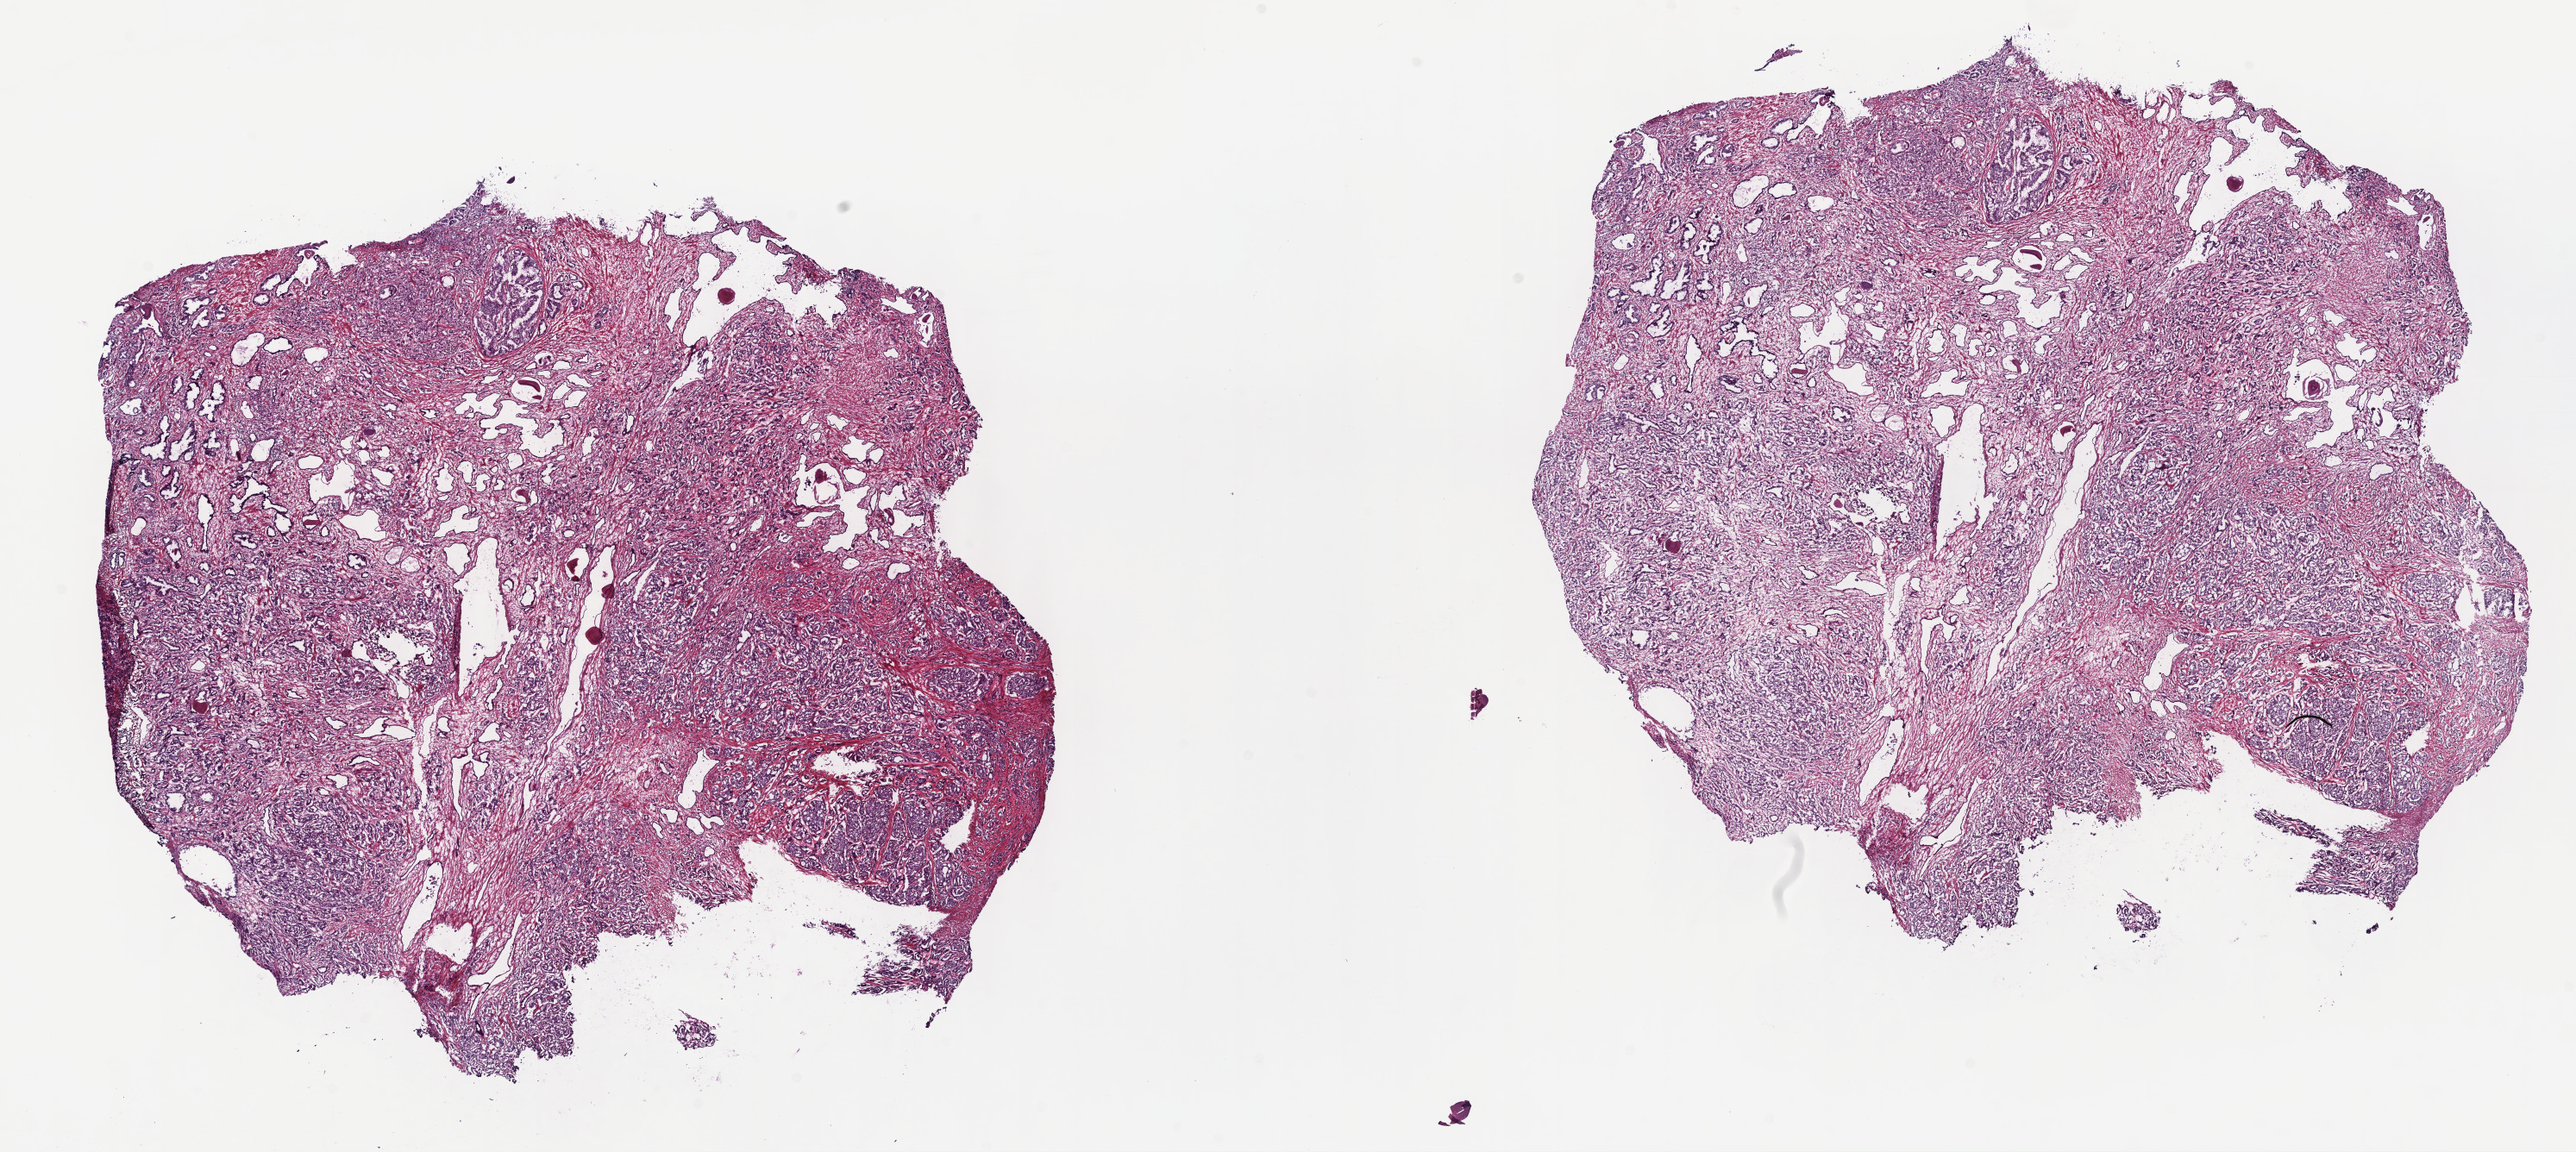
Whole-slide histology image, H&E, shown as a low-resolution overview of the whole scanned area (about 24.2 x 10.8 mm, slide scanned at 40x), frozen section from the top of the tissue portion, sample: primary tumour, prostate. Male patient; age at initial diagnosis 61 years. Gleason score: 8 (4+4). Composition of this section per pathologist review: tumour cells 80%, tumour nuclei 80%, normal cells 0%, stromal cells 20%, necrosis 0%. Inflammatory infiltration, as recorded: lymphocyte infiltration 40%, monocyte infiltration 20%, neutrophil infiltration 20%.
Diagnosis: Adenocarcinoma, NOS (prostate gland). Laterality: bilateral.